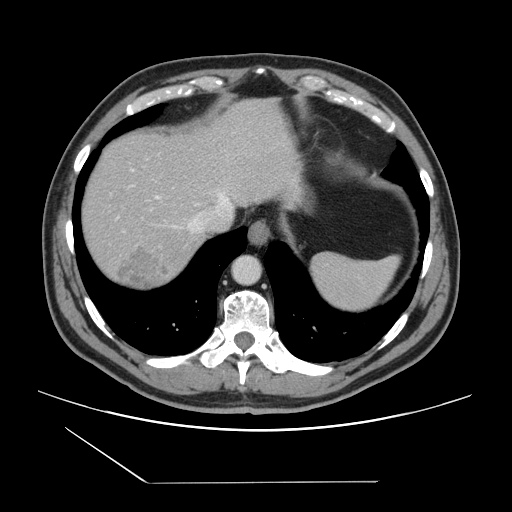
Contrast-enhanced abdominal CT, one axial slice; position 125 of 157 along the scan axis; intravenous contrast given; soft-tissue window (W 400 / L 40 HU); 2.5 mm slice thickness; 512 × 512 image matrix, field of view 407 × 407 mm. Male patient, age 61 years. From the clinical record (not read from this slice): diagnosis: colorectal cancer liver metastases, imaged before liver resection; multiple liver metastases: yes; largest metastasis: 5.5 cm; disease in both lobes: yes.
Structures marked on this image (manually delineated by an expert):
- hepatic veins: bounding box (x1, y1, x2, y2) in pixels: (156, 192, 233, 233)
- liver: (81, 99, 292, 291)
- planned liver remnant (the part of the liver to remain after resection): (82, 111, 233, 230)
- liver metastasis: (114, 247, 173, 289)